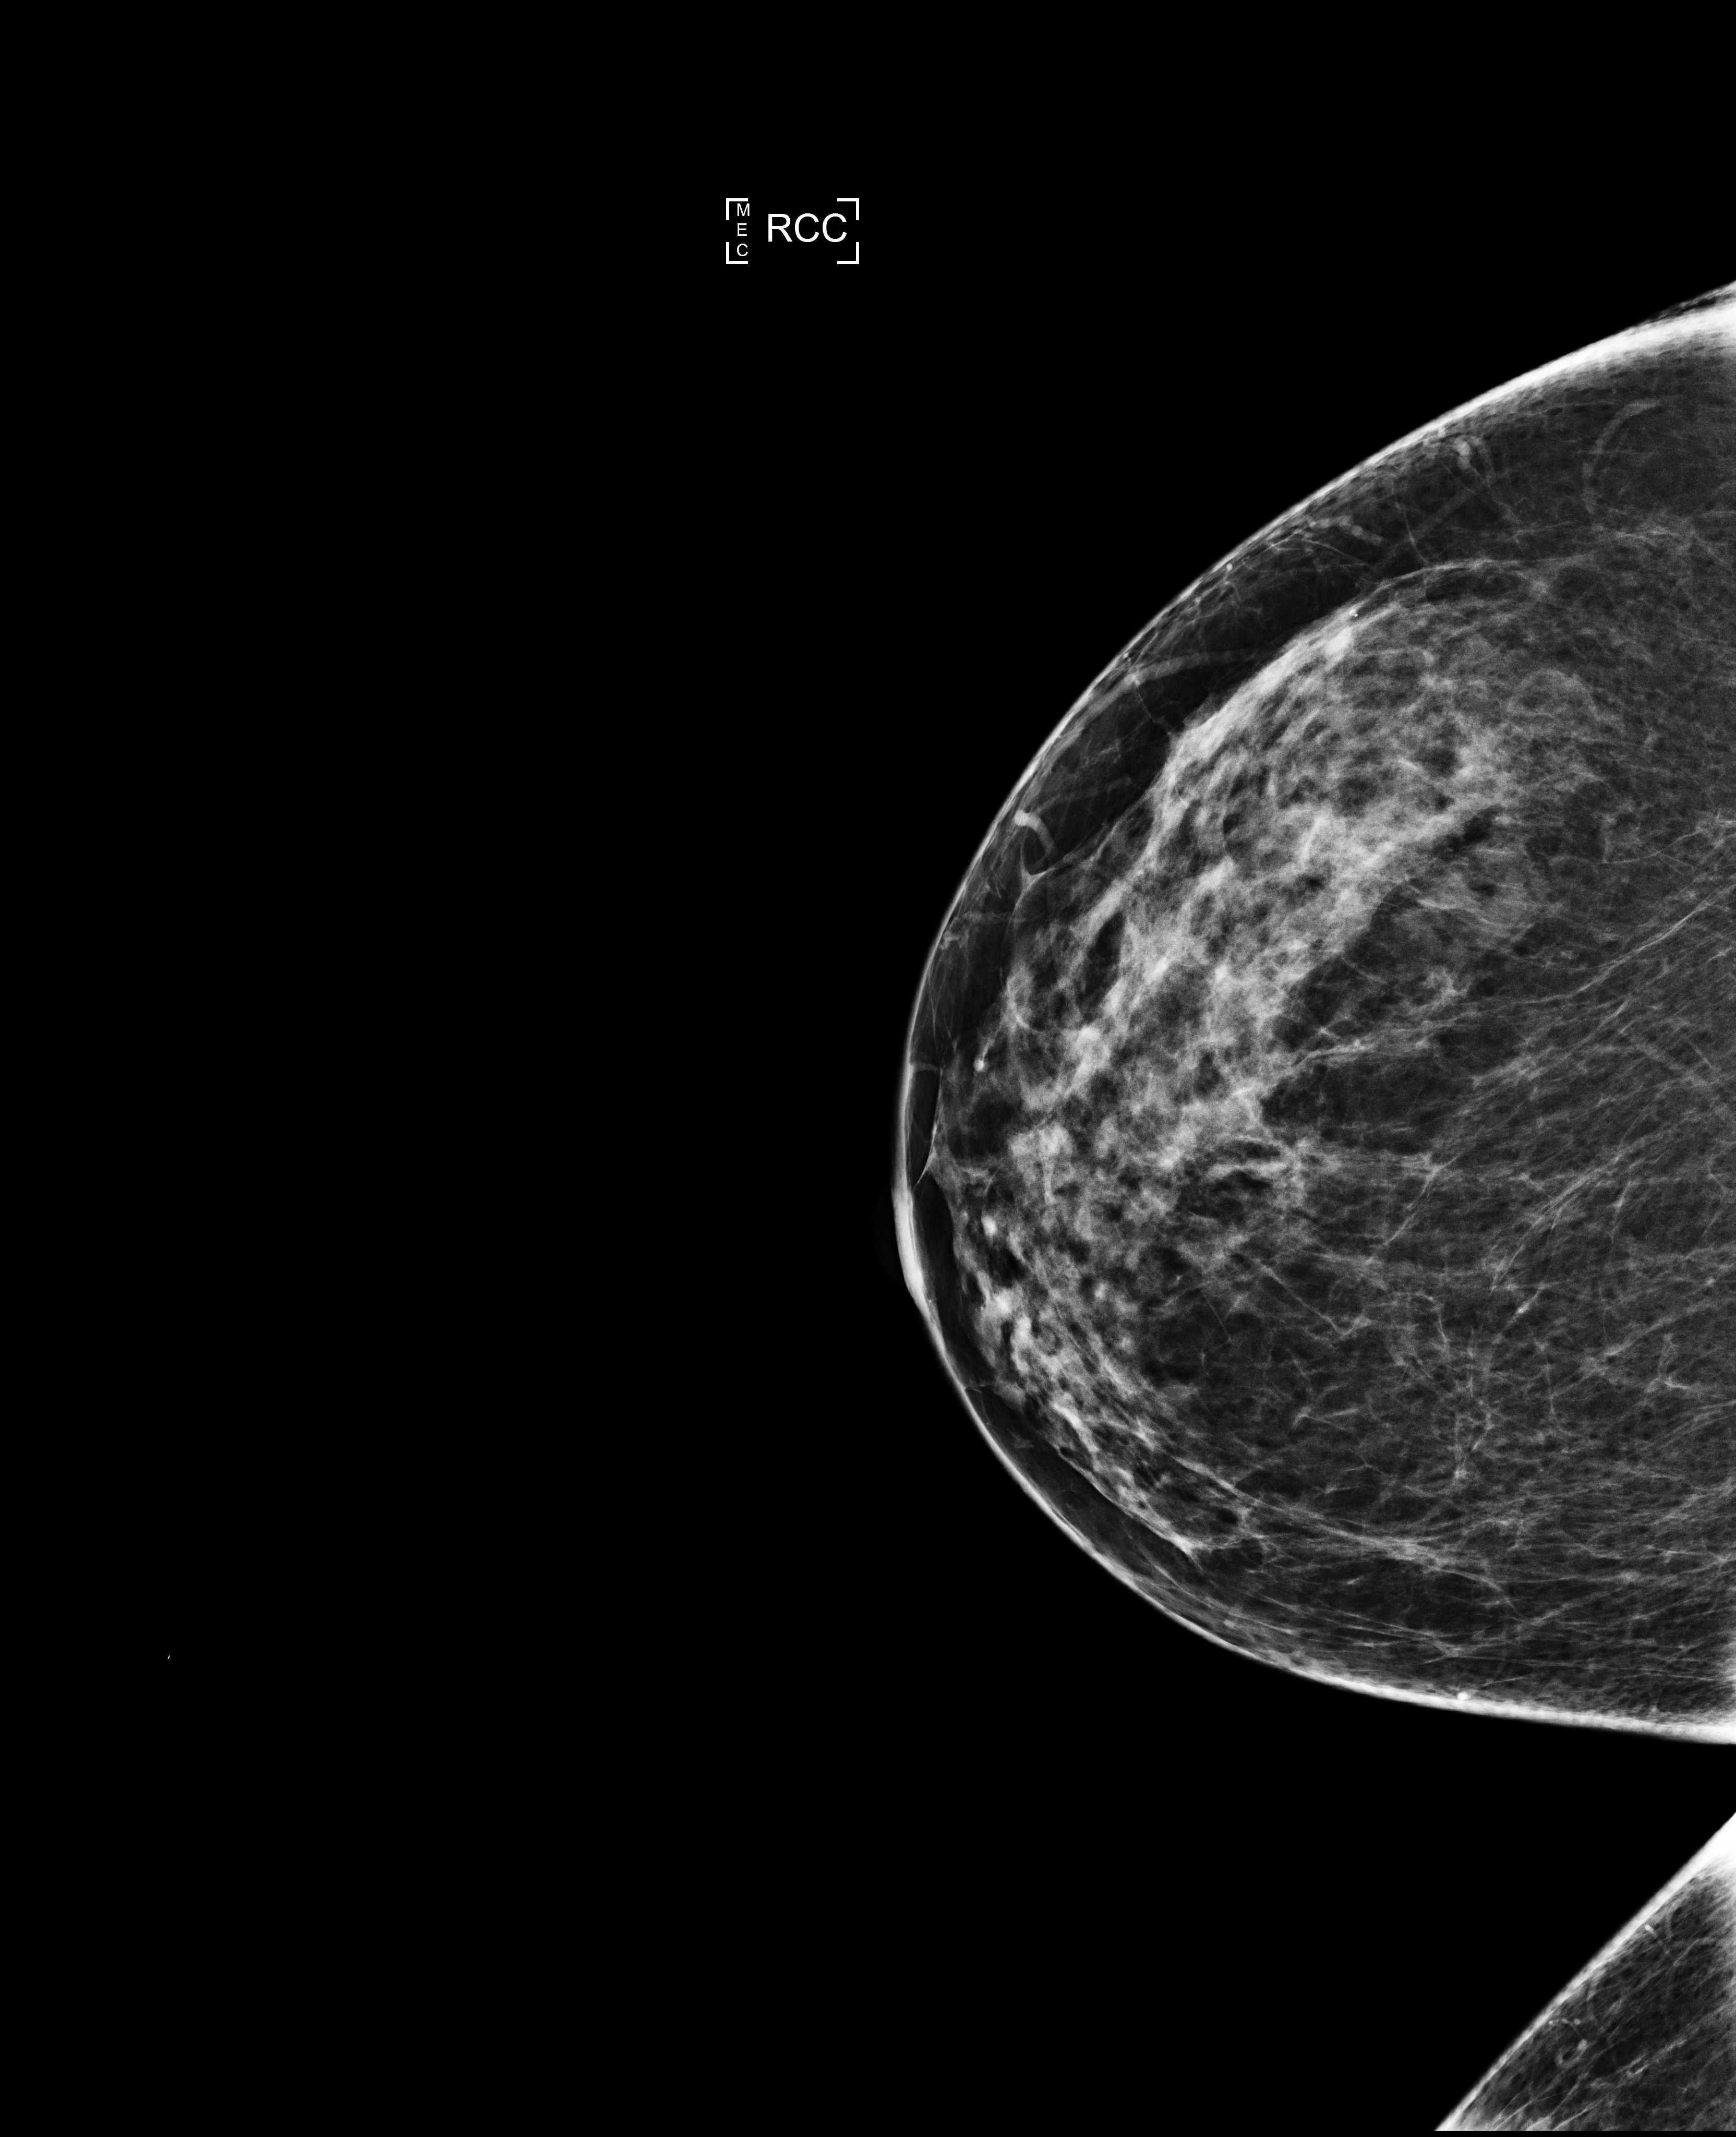
Screening examination. Female patient, age 46 years.
Image type: full-field digital mammogram. Breast: right. Projection: CC view. Breast density at the screening exam (both breasts): heterogeneously dense (BI-RADS density category c). Final BI-RADS assessment for this screening round (tomosynthesis exam, both breasts): category 1. Recall: no recall after this screen.